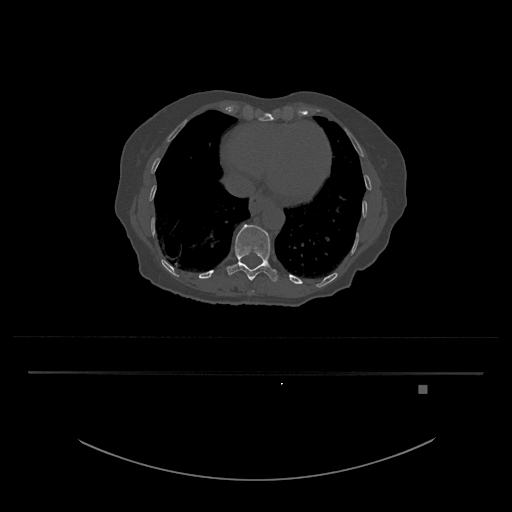
CT including the spine, one axial slice; slice 667 of 797 in the series (ordered by position); reconstruction kernel Br40s/3; bone window (W 1800 / L 400 HU); 512 × 512 image matrix, field of view 500 × 500 mm. Patient: female, 57 years. From the clinical record (not read from this slice): primary cancer: cervical.
Outlined on this slice (semi-automatic segmentation, software-assisted and operator-edited):
- T10 vertebra: box from (x=252, y=290) to (x=254, y=292) px
- T11 vertebra: (x=227, y=224)–(x=278, y=281)